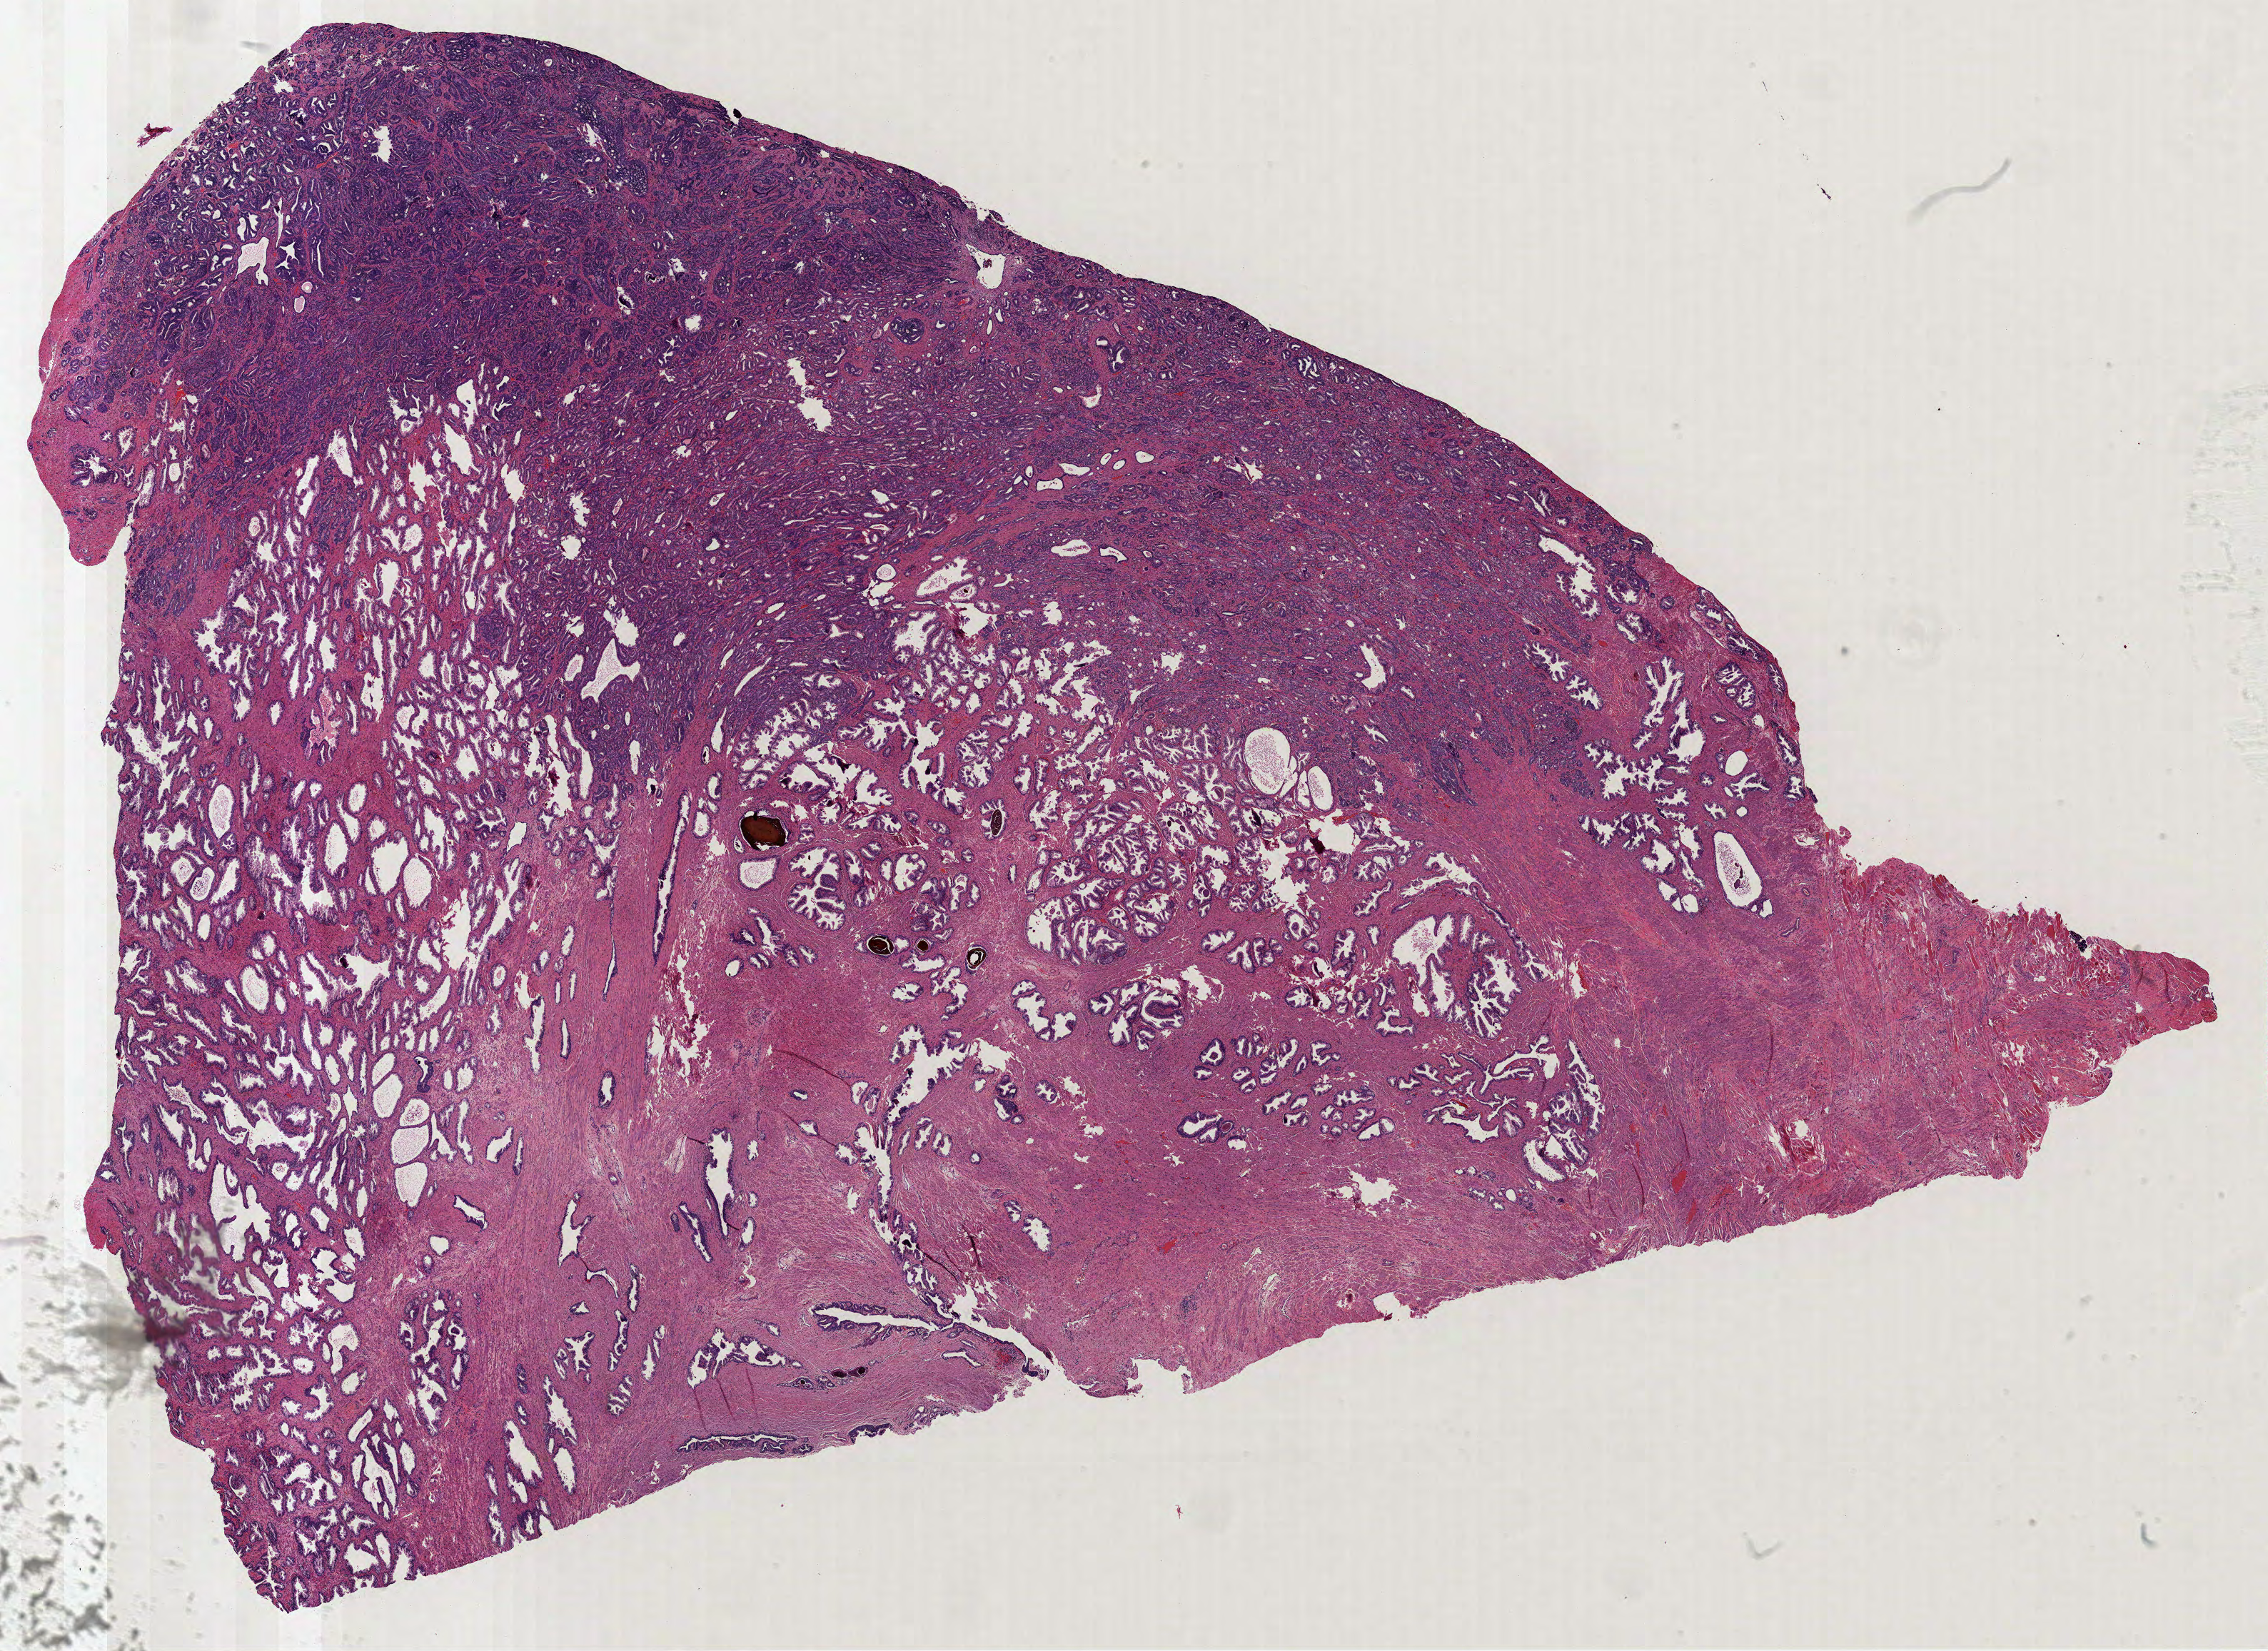
Whole-slide histology image, H&E — a low-resolution overview of the entire scanned area, about 25.6 x 18.7 mm (from a 40x scan). Formalin-fixed paraffin-embedded (FFPE) diagnostic section. Prostate, primary tumour sample. Male patient; age at initial diagnosis 63 years. Gleason score: 7 (4+3).
- laterality: bilateral
- lymph nodes positive (case pathology): 0 of 13 examined
- diagnosis: Acinar cell carcinoma (prostate gland)